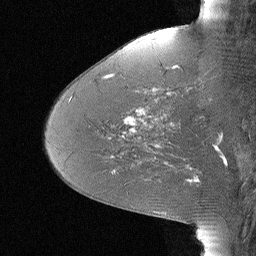
Breast MRI (dynamic contrast-enhanced), one sagittal slice; dynamic contrast-enhanced study with each time point stored as its own series, time point 2 of 3 at this slice position (early post-contrast, ordered by acquisition time); 1.5 T; TE 4 ms, TR 30 ms; 2.25 mm slice thickness; 256 × 256 image matrix, field of view 180 × 180 mm. Female patient, age 46 years. Case-level facts recorded for this patient, not image findings: setting: breast cancer imaged before/during neoadjuvant chemotherapy; receptor status: HR-positive, HER2-negative.
Structures marked on this image (semi-automatic segmentation, software-assisted and operator-edited):
- analysis volume of interest (the breast-tissue region the enhancement analysis was run in; not a lesion): bounding box [x1, y1, x2, y2] px = [106, 43, 184, 119]
- tumour enhancement mask (voxels above the 90 % enhancement threshold inside the analysis volume of interest): [127, 66, 178, 119]